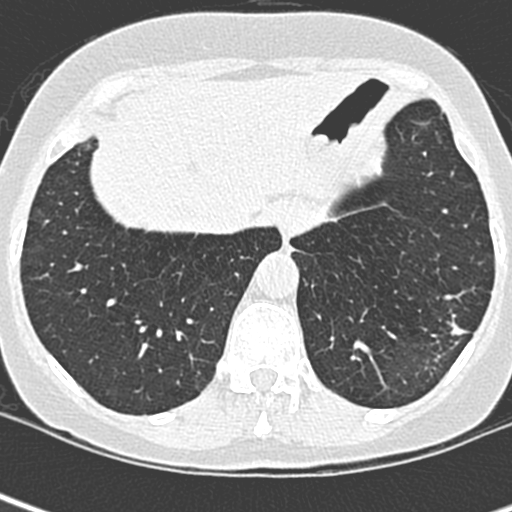
Low-dose screening chest CT, one axial slice; position 65 of 252 along the scan axis; 120 kVp; lung window (W 1500 / L -600 HU); 512 × 512 image matrix, field of view 271 × 271 mm.
Structures marked on this image (outlined manually by an expert reader):
- lesion 1 (tumor, lower lobe of left lung): bounding box <447,319,468,336> (left, top, right, bottom; pixels)